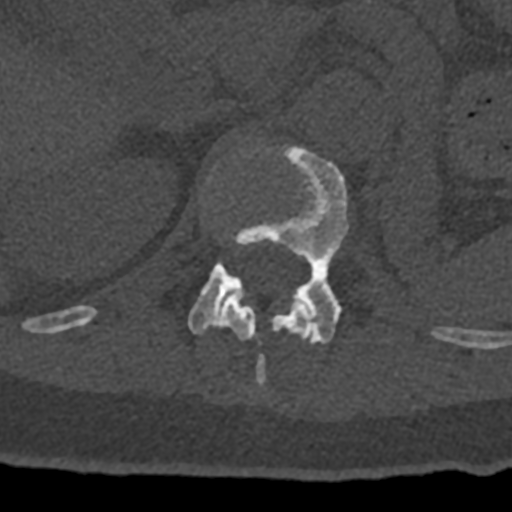
CT including the spine, one axial slice. Slice 460 of 797 in the series (ordered by position). 120 kVp. Bone window (W 1800 / L 400 HU). 0.5 mm slice thickness. 512 × 512 image matrix, field of view 160 × 160 mm. Male patient, age 74 years. Case-level facts recorded for this patient, not image findings: primary cancer: renal; vertebrae with lytic lesions (as recorded): T10, L1, L2, L3, L4, L5.
Outlined on this slice (semi-automatic segmentation, software-assisted and operator-edited):
- L1 vertebra: bounding box (x1, y1, x2, y2) in pixels: (188, 146, 348, 344)
- T12 vertebra: (70, 181, 431, 386)